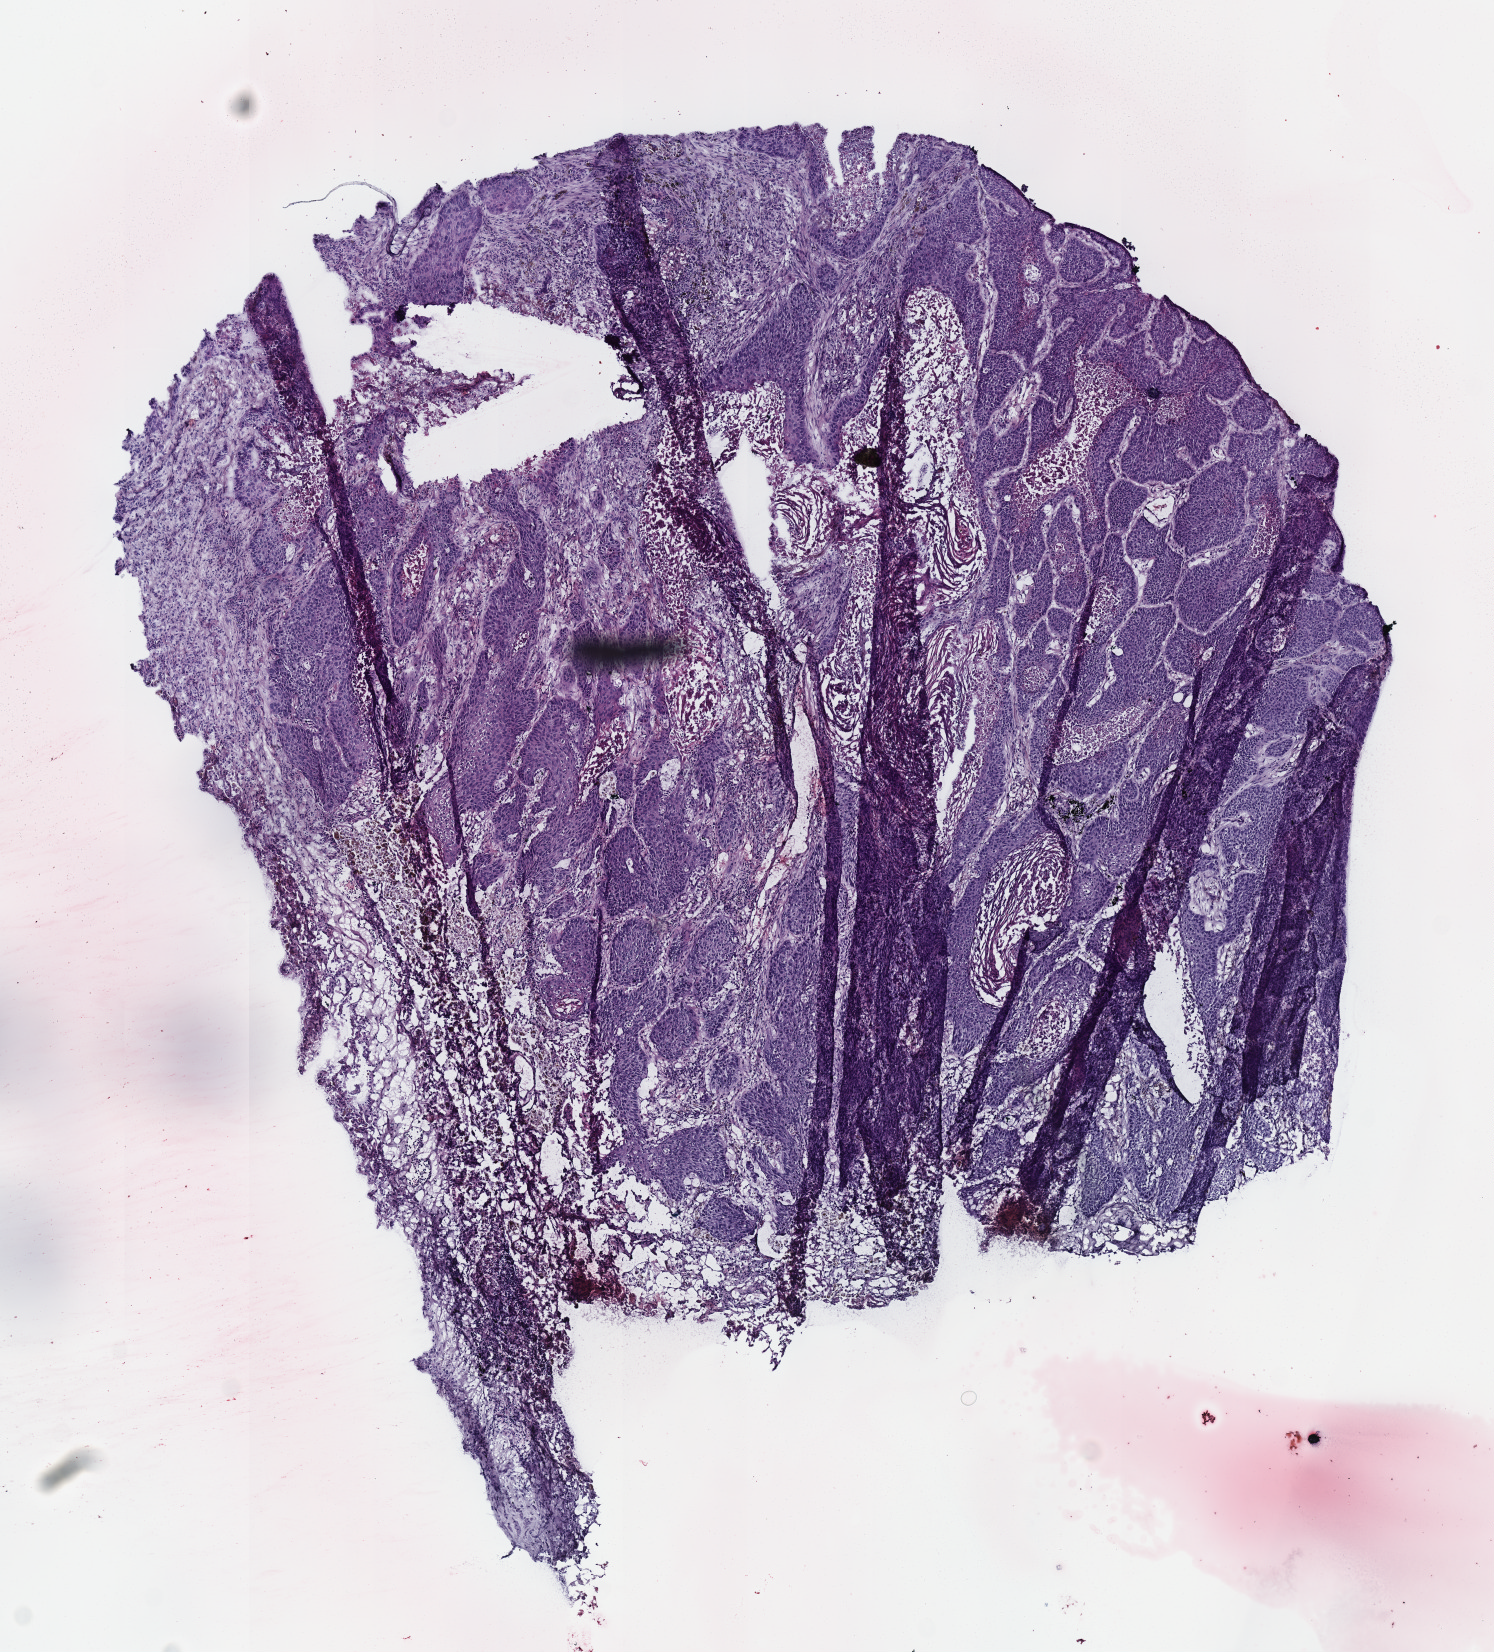
Hematoxylin and eosin (H&E) stained whole-slide image — shown as a low-resolution overview of the whole scanned area (about 5.9 x 6.5 mm, from a 40x scan). Frozen section from the top of the tissue portion. Lung, primary tumour sample. Male patient; age at initial diagnosis 70 years. Pathologist review of this section (percent, as recorded): tumour cells 70%, tumour nuclei 70%.
Histologic diagnosis: Squamous cell carcinoma, NOS (upper lobe, lung).